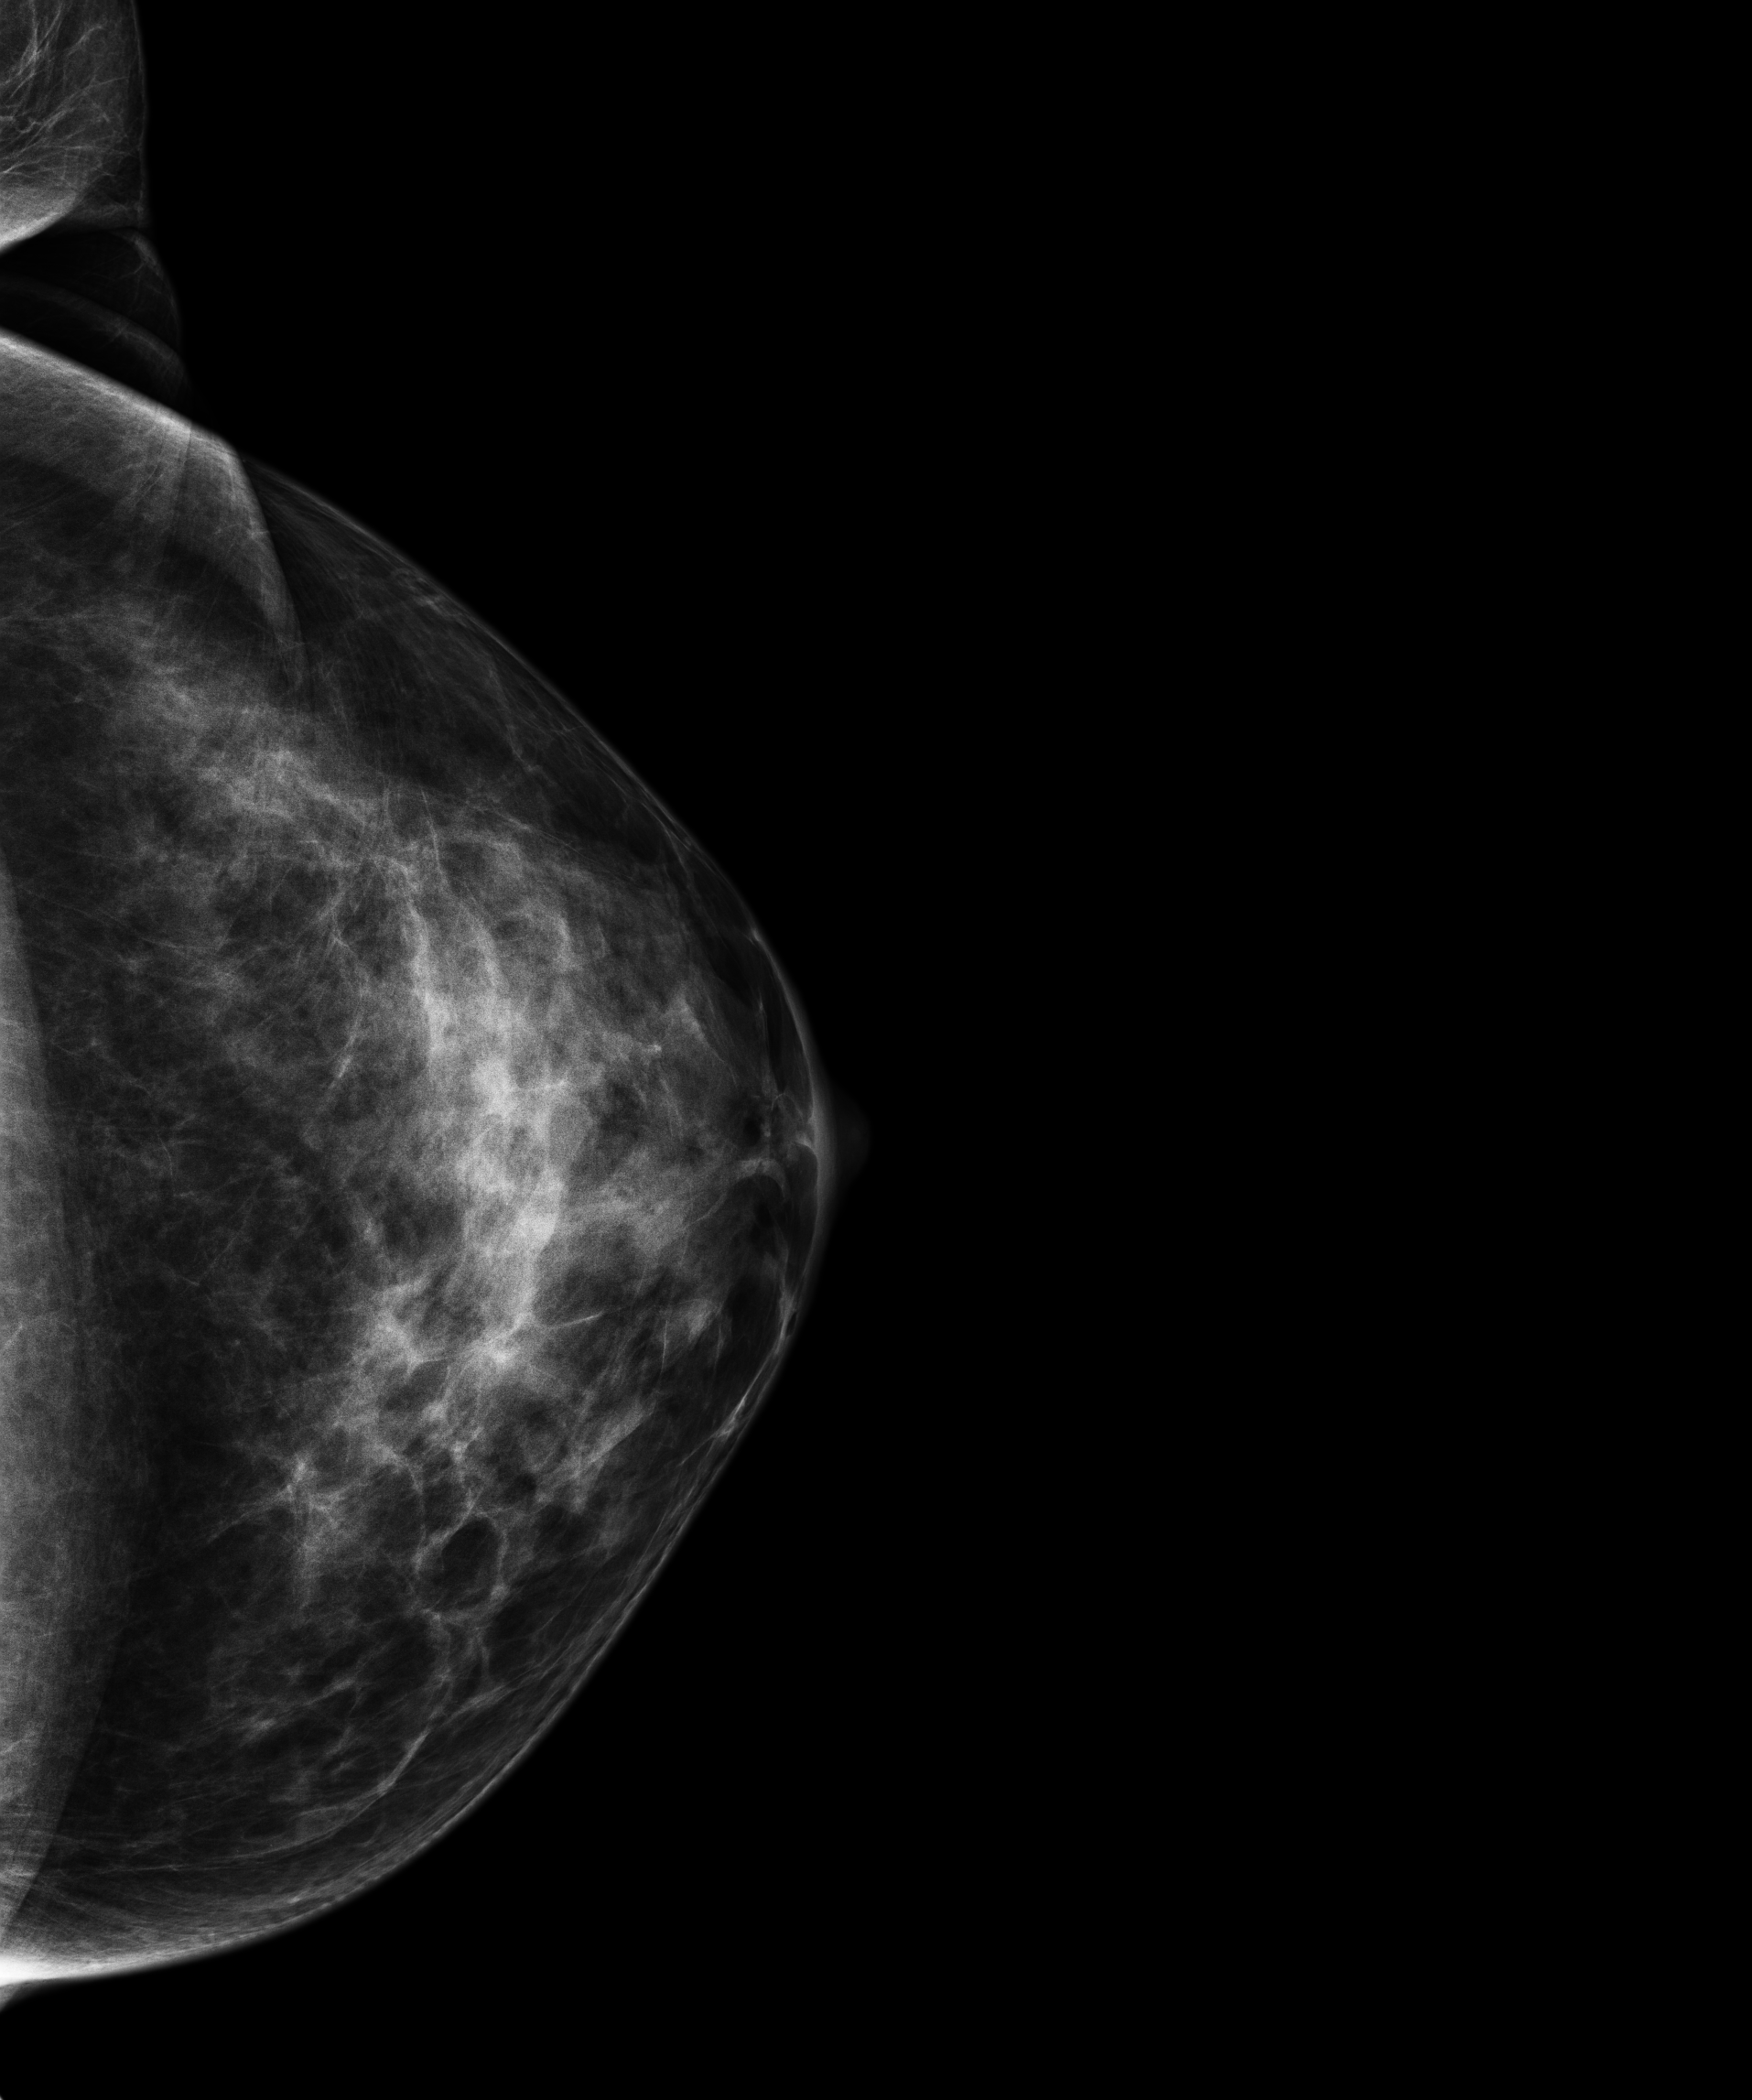
Full-field digital mammogram (FFDM), left breast, craniocaudal (CC) view, annual screening mammography examination, compressed breast thickness 62 mm, system: Senographe Essential ADS_56.21.3. Patient: female, 42 years.
BI-RADS breast density category at the screening exam (both breasts, scale 1–4): 3. Final BI-RADS category for the screening round (tomosynthesis exam, both breasts): category 1. Recall: no recall after this screen.